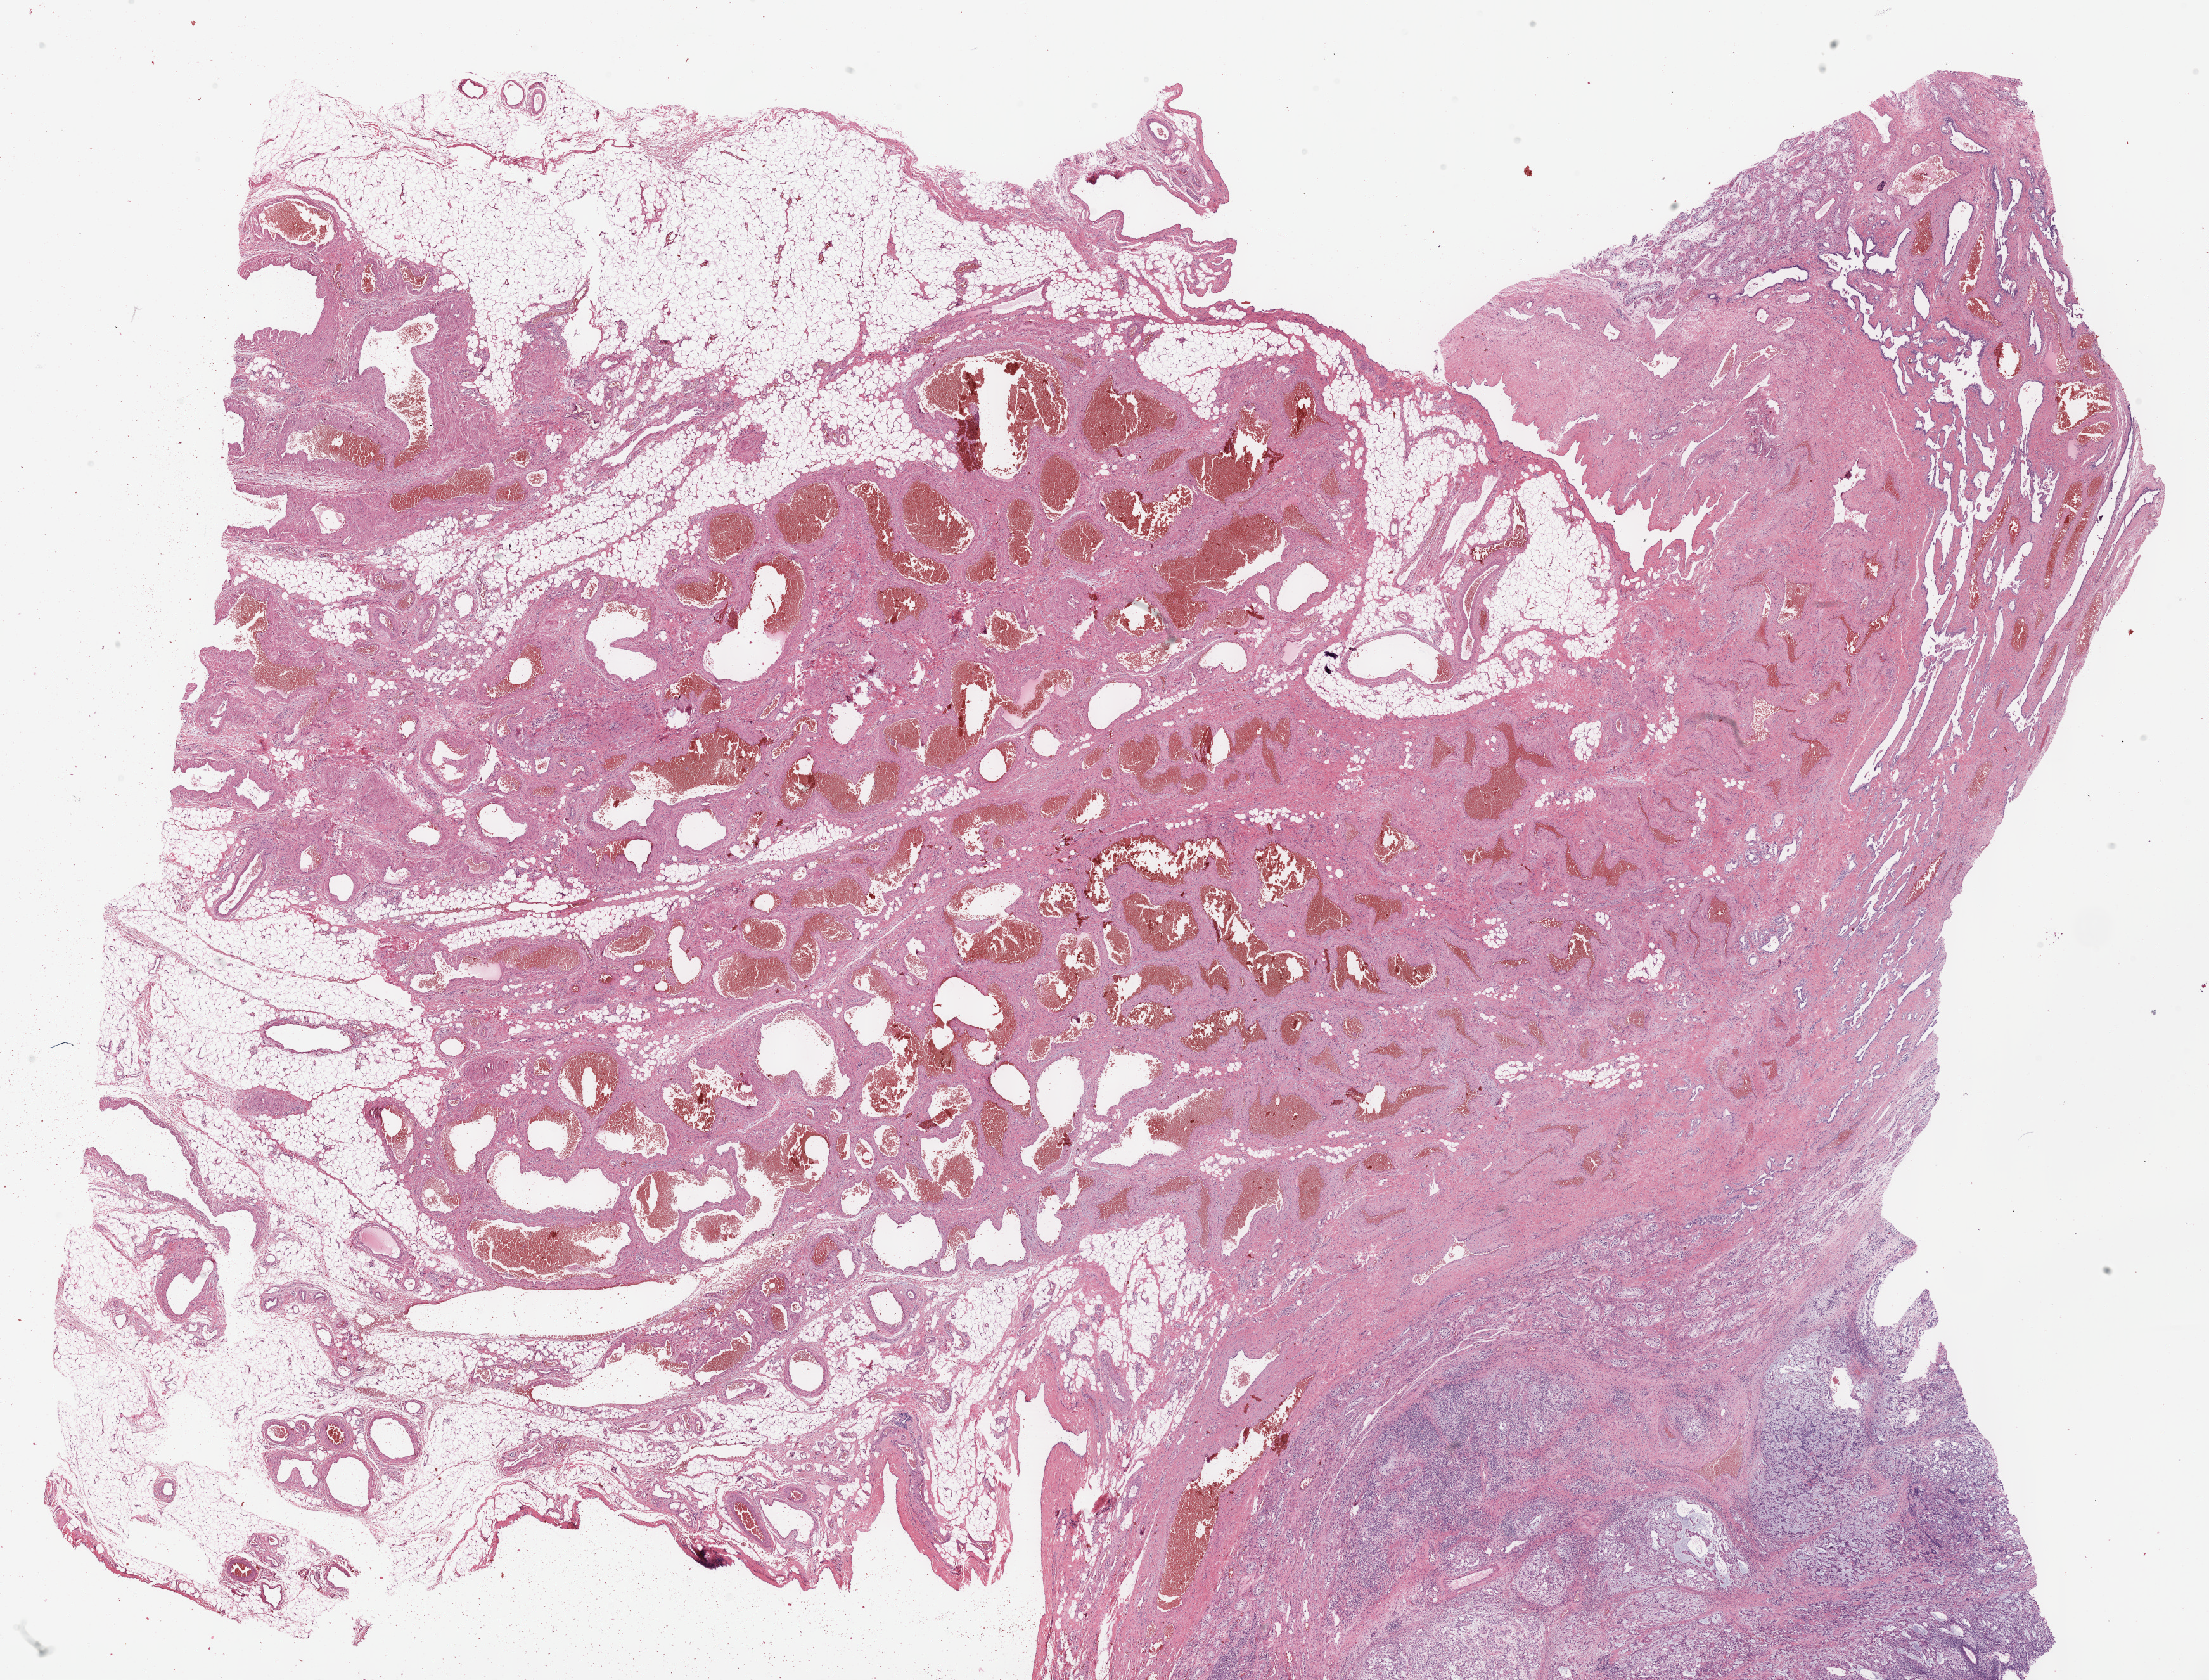
H&E-stained whole-slide image, a low-resolution overview of the entire scanned area, about 28.2 x 21.4 mm. Formalin-fixed paraffin-embedded (FFPE) diagnostic section. Testis, primary tumour sample. Patient: male, age at initial diagnosis 29 years.
AJCC pathologic stage: IS (7th edition). Laterality: left. Diagnosis: Mixed germ cell tumor.